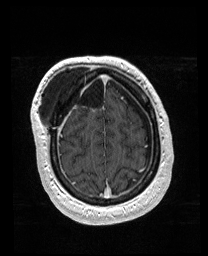
Brain MRI from a brain-tumour surgery series, one axial slice. Slice 42 of 176 in the series (ordered by position). T1-weighted post-contrast. 208 × 256 image matrix, field of view 208 × 256 mm. Case-level facts recorded for this patient, not image findings: histopathology: Astrocytoma; WHO grade: 4; IDH mutation: yes.
Outlined on this slice (outlined manually by an expert reader):
- previous resection cavity: bounding box [x1, y1, x2, y2] px = [76, 74, 103, 107]